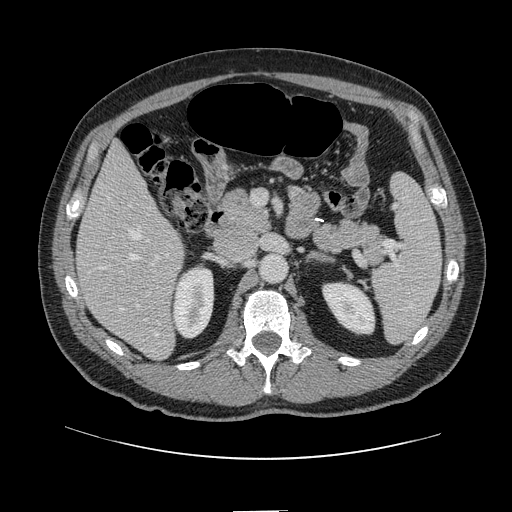
Contrast-enhanced abdominal CT, one axial slice; slice 58 of 161 in the series (ordered by position); 120 kVp; intravenous contrast given; soft-tissue window (W 400 / L 40 HU); 512 × 512 image matrix, field of view 412 × 412 mm. Male patient, age 66 years. Case-level facts recorded for this patient, not image findings: diagnosis: colorectal cancer liver metastases, imaged before liver resection; multiple liver metastases: no; largest metastasis: 3.5 cm.
Annotated regions visible in this slice (manually delineated by an expert):
- hepatic veins: bounding box [x1, y1, x2, y2] px = [109, 198, 158, 336]
- liver: [77, 144, 184, 359]
- planned liver remnant (the part of the liver to remain after resection): [77, 144, 169, 282]
- portal vein (with intrahepatic branches): [147, 255, 161, 295]